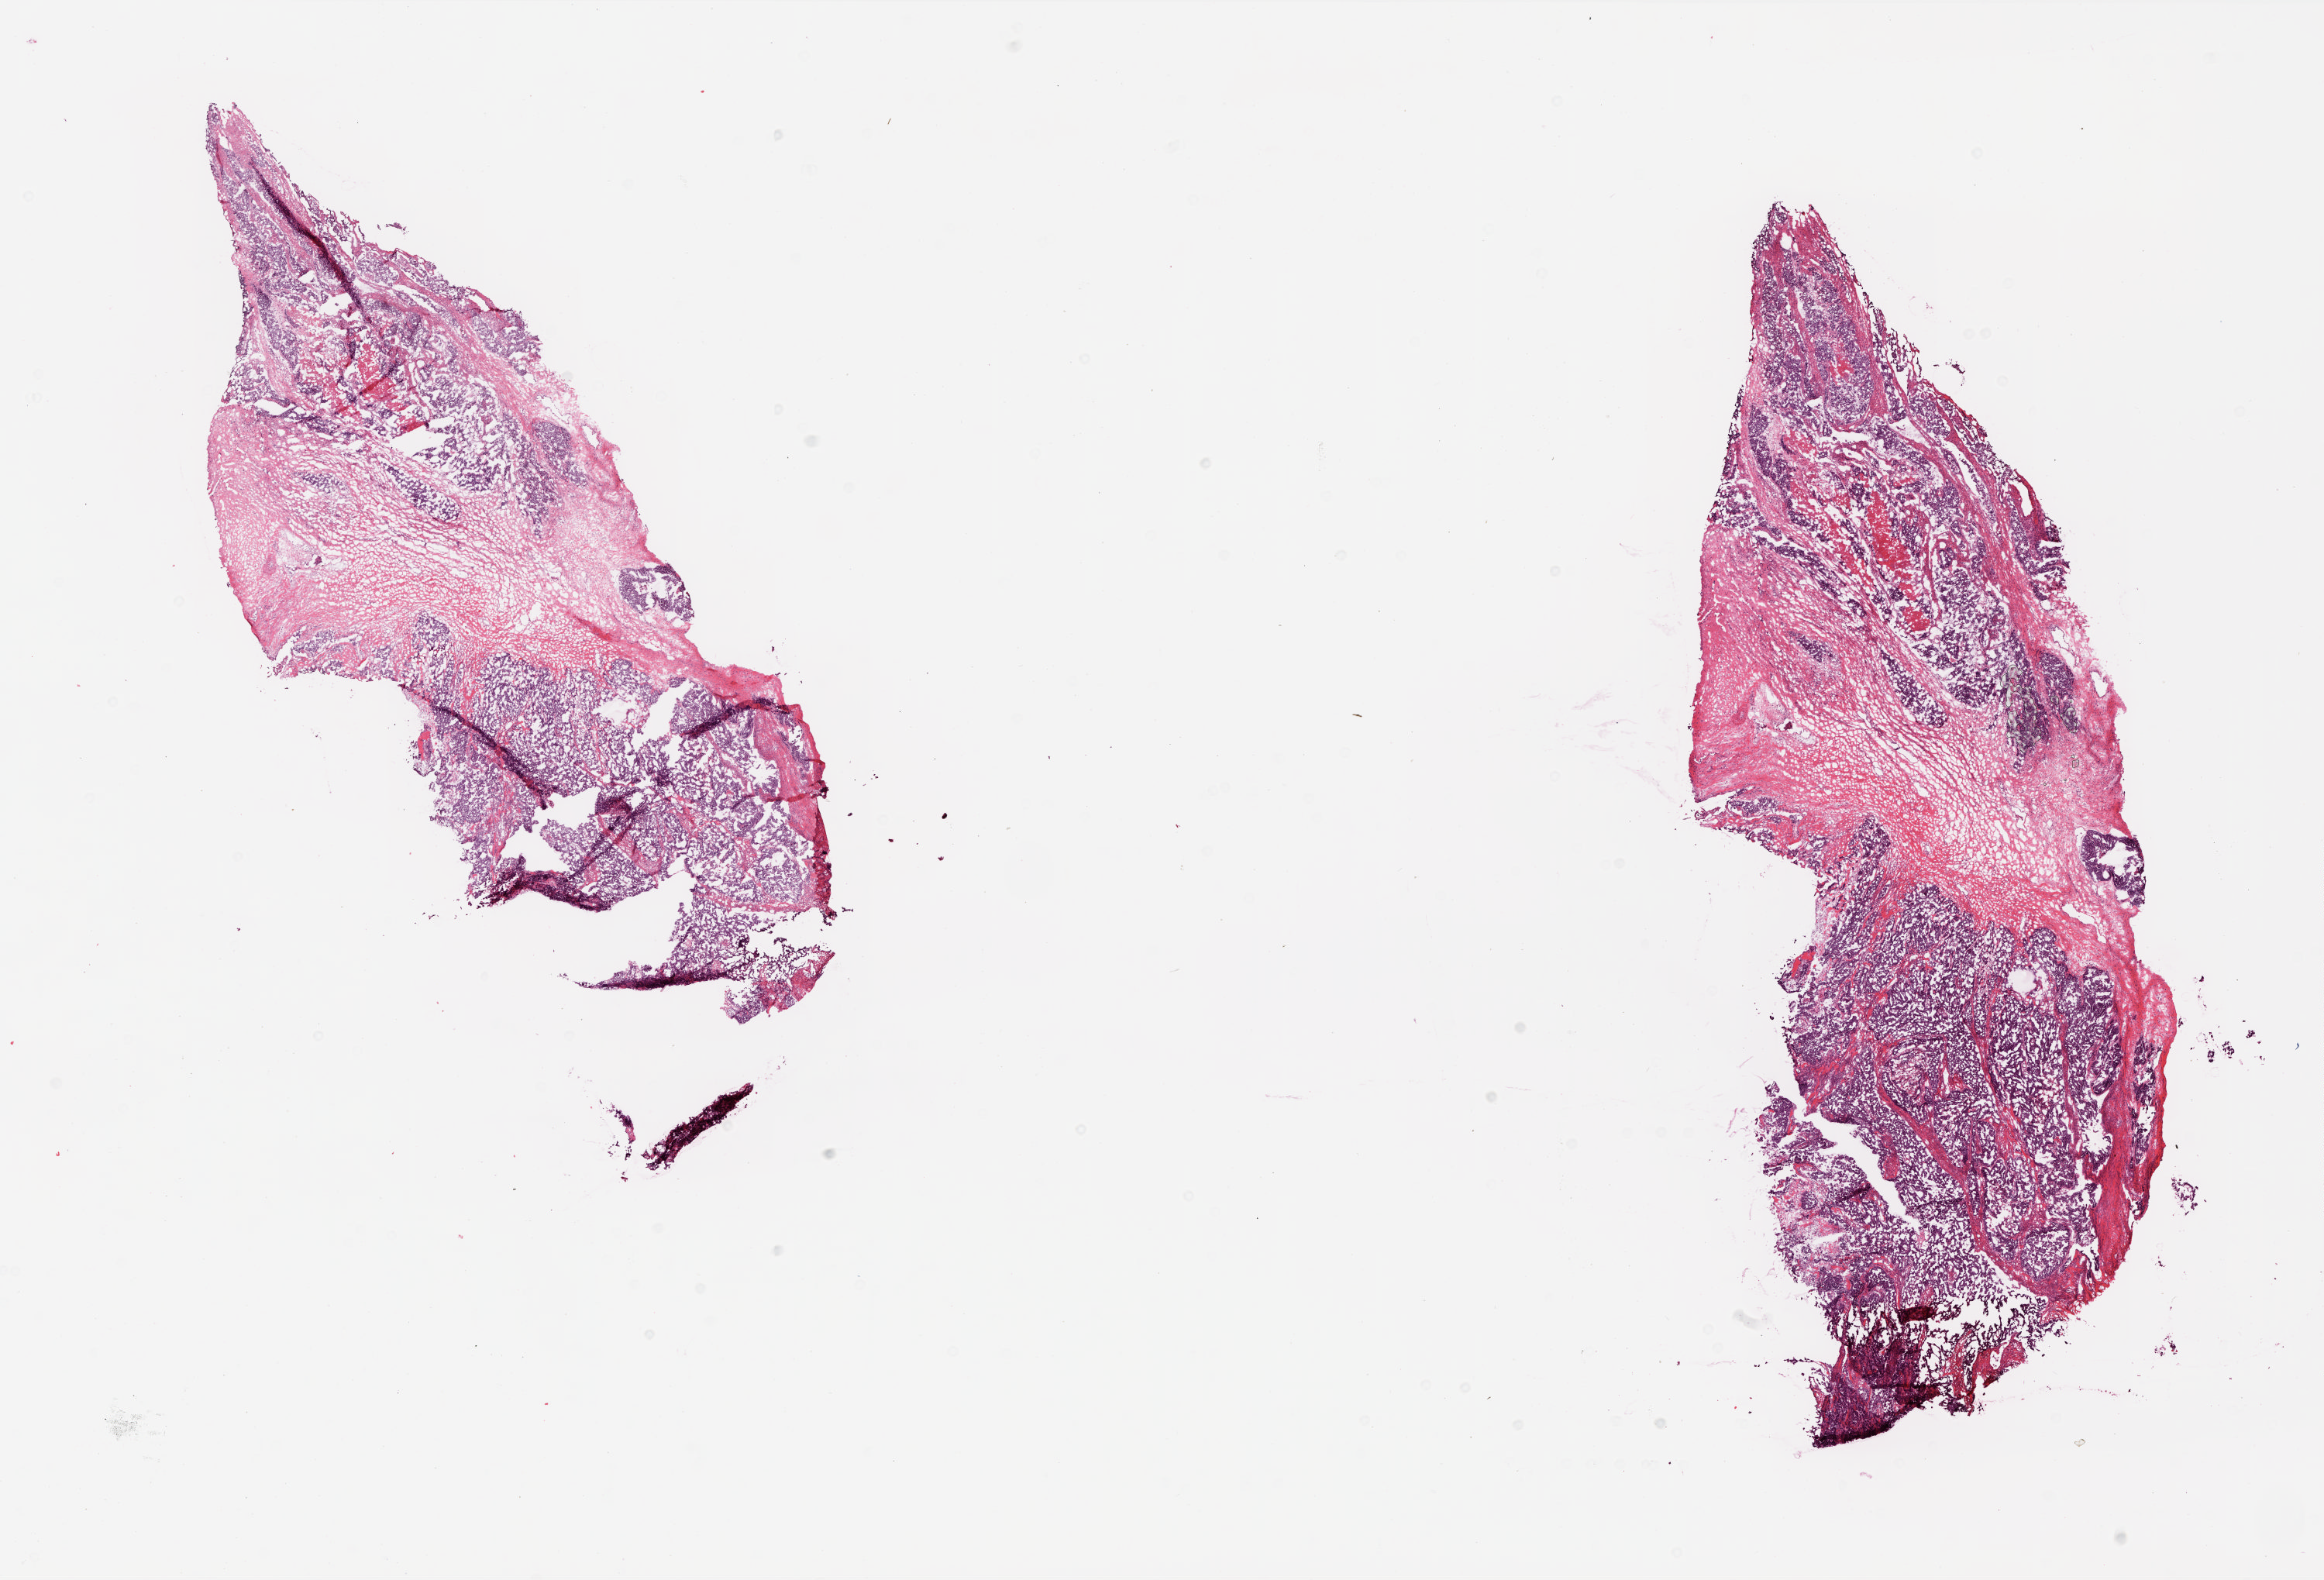
Whole-slide histology image, H&E, shown as a low-resolution overview of the whole scanned area (about 24.0 x 16.3 mm). Frozen section. Ovary, primary tumour sample. Female, age 76 years at initial diagnosis. Histologic grade: G2 (moderately differentiated). Slide review estimates, as recorded: tumour cells 55%, tumour nuclei 90%, normal cells 0%, stromal cells 30%, necrosis 15%.
Diagnosis: Serous cystadenocarcinoma, NOS. FIGO stage: IIIC.